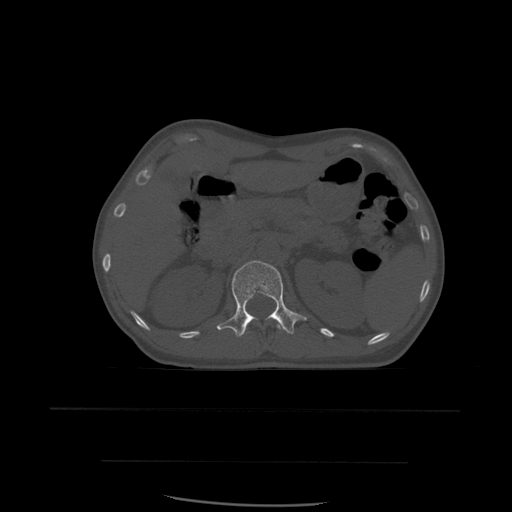
CT including the spine, one axial slice; position 253 of 574 along the scan axis; bone window (W 1800 / L 400 HU); 1.25 mm slice thickness; 512 × 512 image matrix, field of view 392 × 392 mm. Patient age 48 years. From the clinical record (not read from this slice): primary cancer: lung; vertebrae with lytic lesions (as recorded): T11.
Annotated regions visible in this slice (semi-automatic segmentation, software-assisted and operator-edited):
- L1 vertebra: box from (x=217, y=261) to (x=307, y=338) px
- T12 vertebra: (x=247, y=324)–(x=281, y=330)